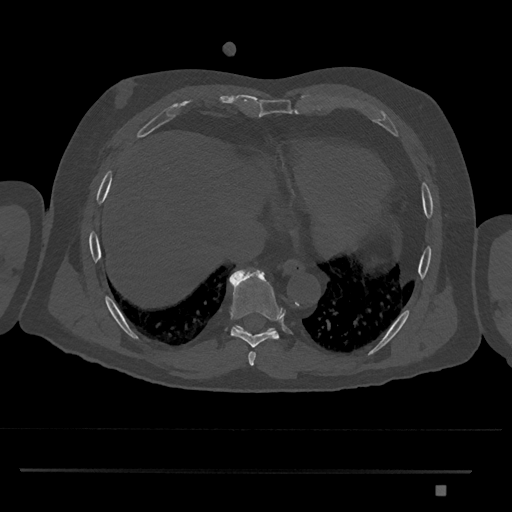
CT including the spine, one axial slice. Slice 1101 of 1134 in the series (ordered by position). Reconstruction kernel Br40s/3. Bone window (W 1800 / L 400 HU). 0.5 mm slice thickness. 512 × 512 image matrix, field of view 429 × 429 mm. Patient: male, 65 years. From the clinical record (not read from this slice): primary cancer: prostate.
Annotated regions visible in this slice (semi-automatic segmentation, software-assisted and operator-edited):
- T8 vertebra: bounding box <229,269,283,347> (left, top, right, bottom; pixels)
- T9 vertebra: <235,325,275,332>